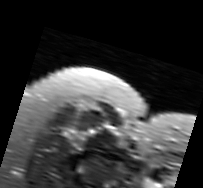
MRI of an extremity soft-tissue mass, one axial slice; slice 70 of 91 in the series (ordered by position); T2-weighted fat-saturated; MR volume resampled by the dataset authors to the PET/CT grid (not the native acquisition matrix); 3.27 mm slice thickness; 203 × 188 image matrix. Female patient. From the clinical record (not read from this slice): histological type: malignant solitary fibrous tumor; grade: intermediate; site of the primary tumour: right thigh.
Structures marked on this image (expert contour drawn on MRI and transferred to this co-registered scan by the dataset authors):
- gross tumour volume including surrounding oedema: box from (x=69, y=126) to (x=95, y=148) px